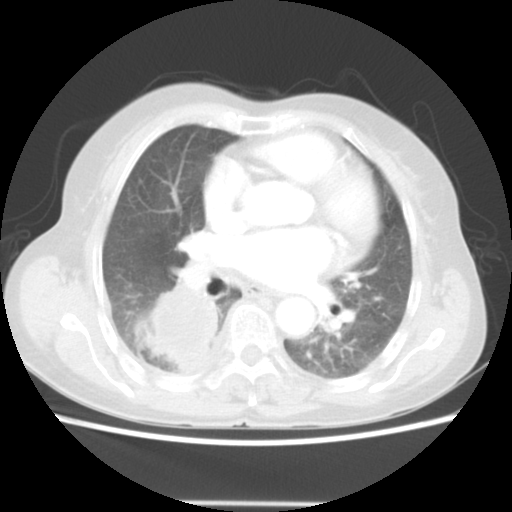
Chest CT, one axial slice; slice 26 of 52 in the series (ordered by position); 140 kVp; lung window (W 1500 / L -600 HU); 5 mm slice thickness; 512 × 512 image matrix, field of view 337 × 337 mm. Patient: female, 67 years. From the clinical record (not read from this slice): clinical TNM (as recorded): T3 N1 M1.
Outlined on this slice (rectangle marked by the reading radiologist):
- lung tumour (recorded histology: adenocarcinoma): bounding box (x1, y1, x2, y2) in pixels: (137, 280, 227, 366)